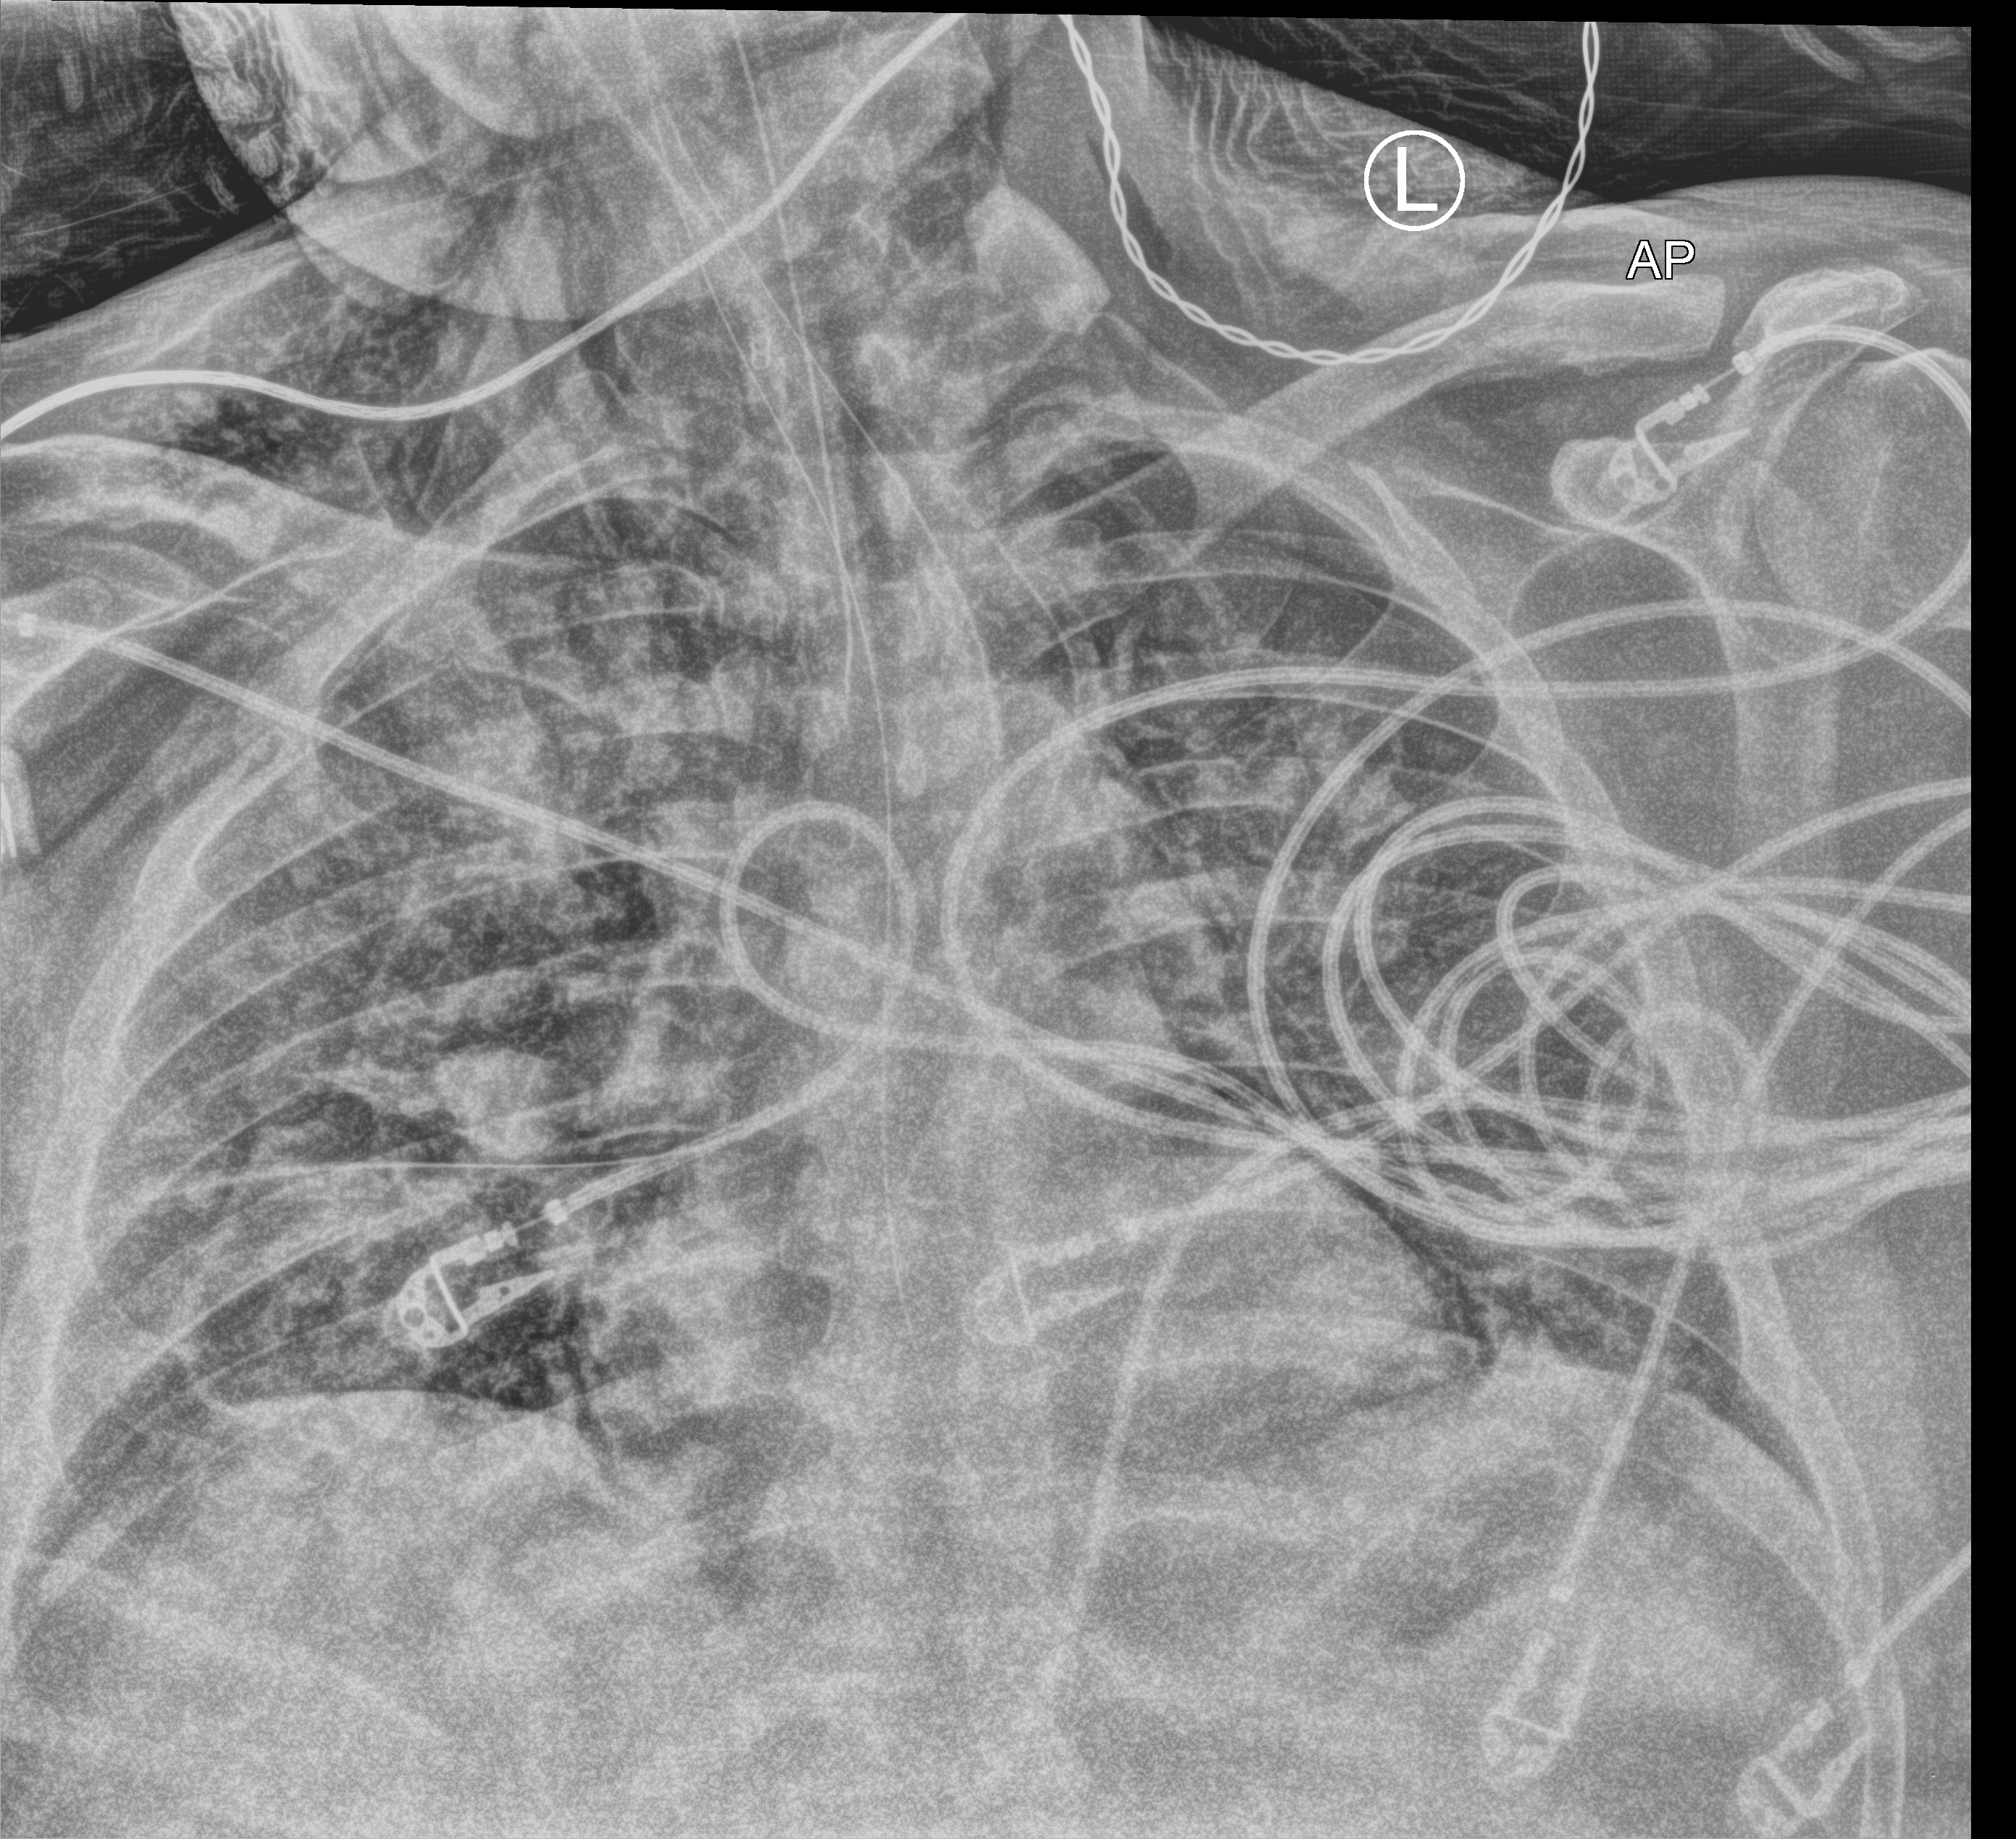
Portable chest radiograph. Patient hospitalised with COVID-19, aged 18–59 years.
Hospital-stay facts (about this admission, not read from this image; timing relative to this image not recorded): mechanically ventilated during this hospital stay: yes.